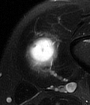
MRI of an extremity soft-tissue mass, one axial slice. Position 16 of 65 along the scan axis. T2-weighted fat-saturated. MR volume resampled by the dataset authors to the PET/CT grid (not the native acquisition matrix). 3.27 mm slice thickness. 90 × 105 image matrix, field of view 88 × 103 mm. Male patient. From the clinical record (not read from this slice): histological type: mixoid liposarcoma; grade: low; site of the primary tumour: left thigh.
Outlined on this slice (expert contour drawn on MRI and transferred to this co-registered scan by the dataset authors):
- gross tumour volume (mass): box from (x=23, y=34) to (x=58, y=72) px